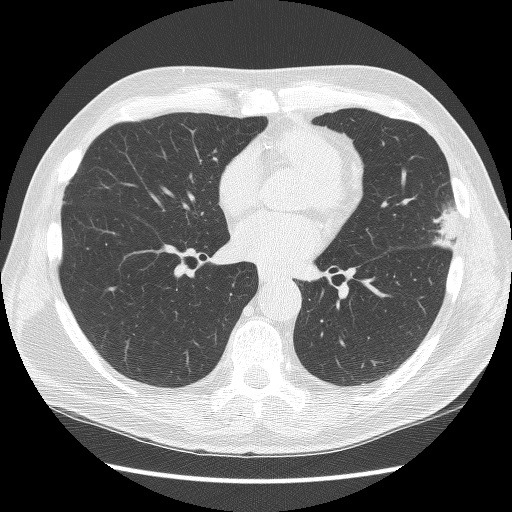
Chest CT (low-dose screening protocol), one axial image, third screening round (two years after baseline), lung window (W 1500 / L -600 HU), lung (sharp) reconstruction kernel (BONE), 512 × 512 image matrix. Male participant, aged 67 years at enrolment.
- Expert-annotated lung lesion, bounding box <409,193,473,265> (left, top, right, bottom; pixels).
- The exam's reader record, not a measurement of the box and not confirmed to be the same lesion: non-calcified nodule or mass ≥4 mm, left upper lobe, 22 × 17 mm, poorly defined margins, soft tissue attenuation, pre-existing on the prior screen: yes; interval growth: yes.
- Later outcome: lung cancer diagnosed 72 days after this screen — squamous cell carcinoma, NOS, left upper lobe, moderately differentiated (G2), stage IB (AJCC 6th edition), 25 mm at pathology.